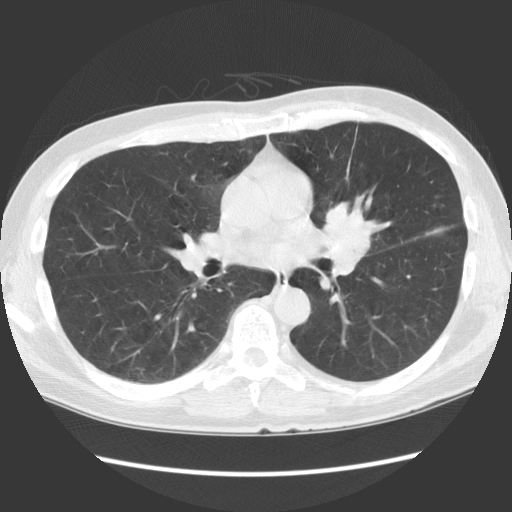
Axial slice from a low-dose chest CT screening exam. Baseline annual screen. Lung window (W 1500 / L -600 HU). Standard (soft-tissue) reconstruction kernel (STANDARD). Male, age 61 years at enrolment. Former smoker at enrolment.
Lesion marked by an expert reader, box from (x=294, y=193) to (x=392, y=294) px. The exam's reader record, not a measurement of the box and not confirmed to be the same lesion: non-calcified nodule or mass ≥4 mm, lingula, 35 × 35 mm, spiculated (stellate) margins, soft tissue attenuation. Official screen result: positive, change unspecified: nodule(s) >= 4 mm or enlarging nodule(s), mass(es), or other non-specific abnormalities suspicious for lung cancer.